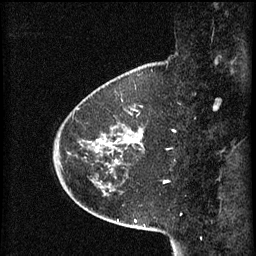
Breast MRI (dynamic contrast-enhanced), one sagittal slice. Slice 17 of 60 in the series (ordered by position). 3 images stored at this slice position (order not interpretable as contrast timing). 1.5 T. TE 4.2 ms, TR 8.2 ms. 2 mm slice thickness. 256 × 256 image matrix, field of view 200 × 200 mm. Female patient, age 45 years.
Outlined on this slice (semi-automatically segmented with operator editing):
- analysis volume of interest (the breast-tissue region the enhancement analysis was run in; not a lesion): bounding box <80,102,144,171> (left, top, right, bottom; pixels)
- tumour enhancement mask (voxels above the 70 % enhancement threshold inside the analysis volume of interest): <107,142,143,163>